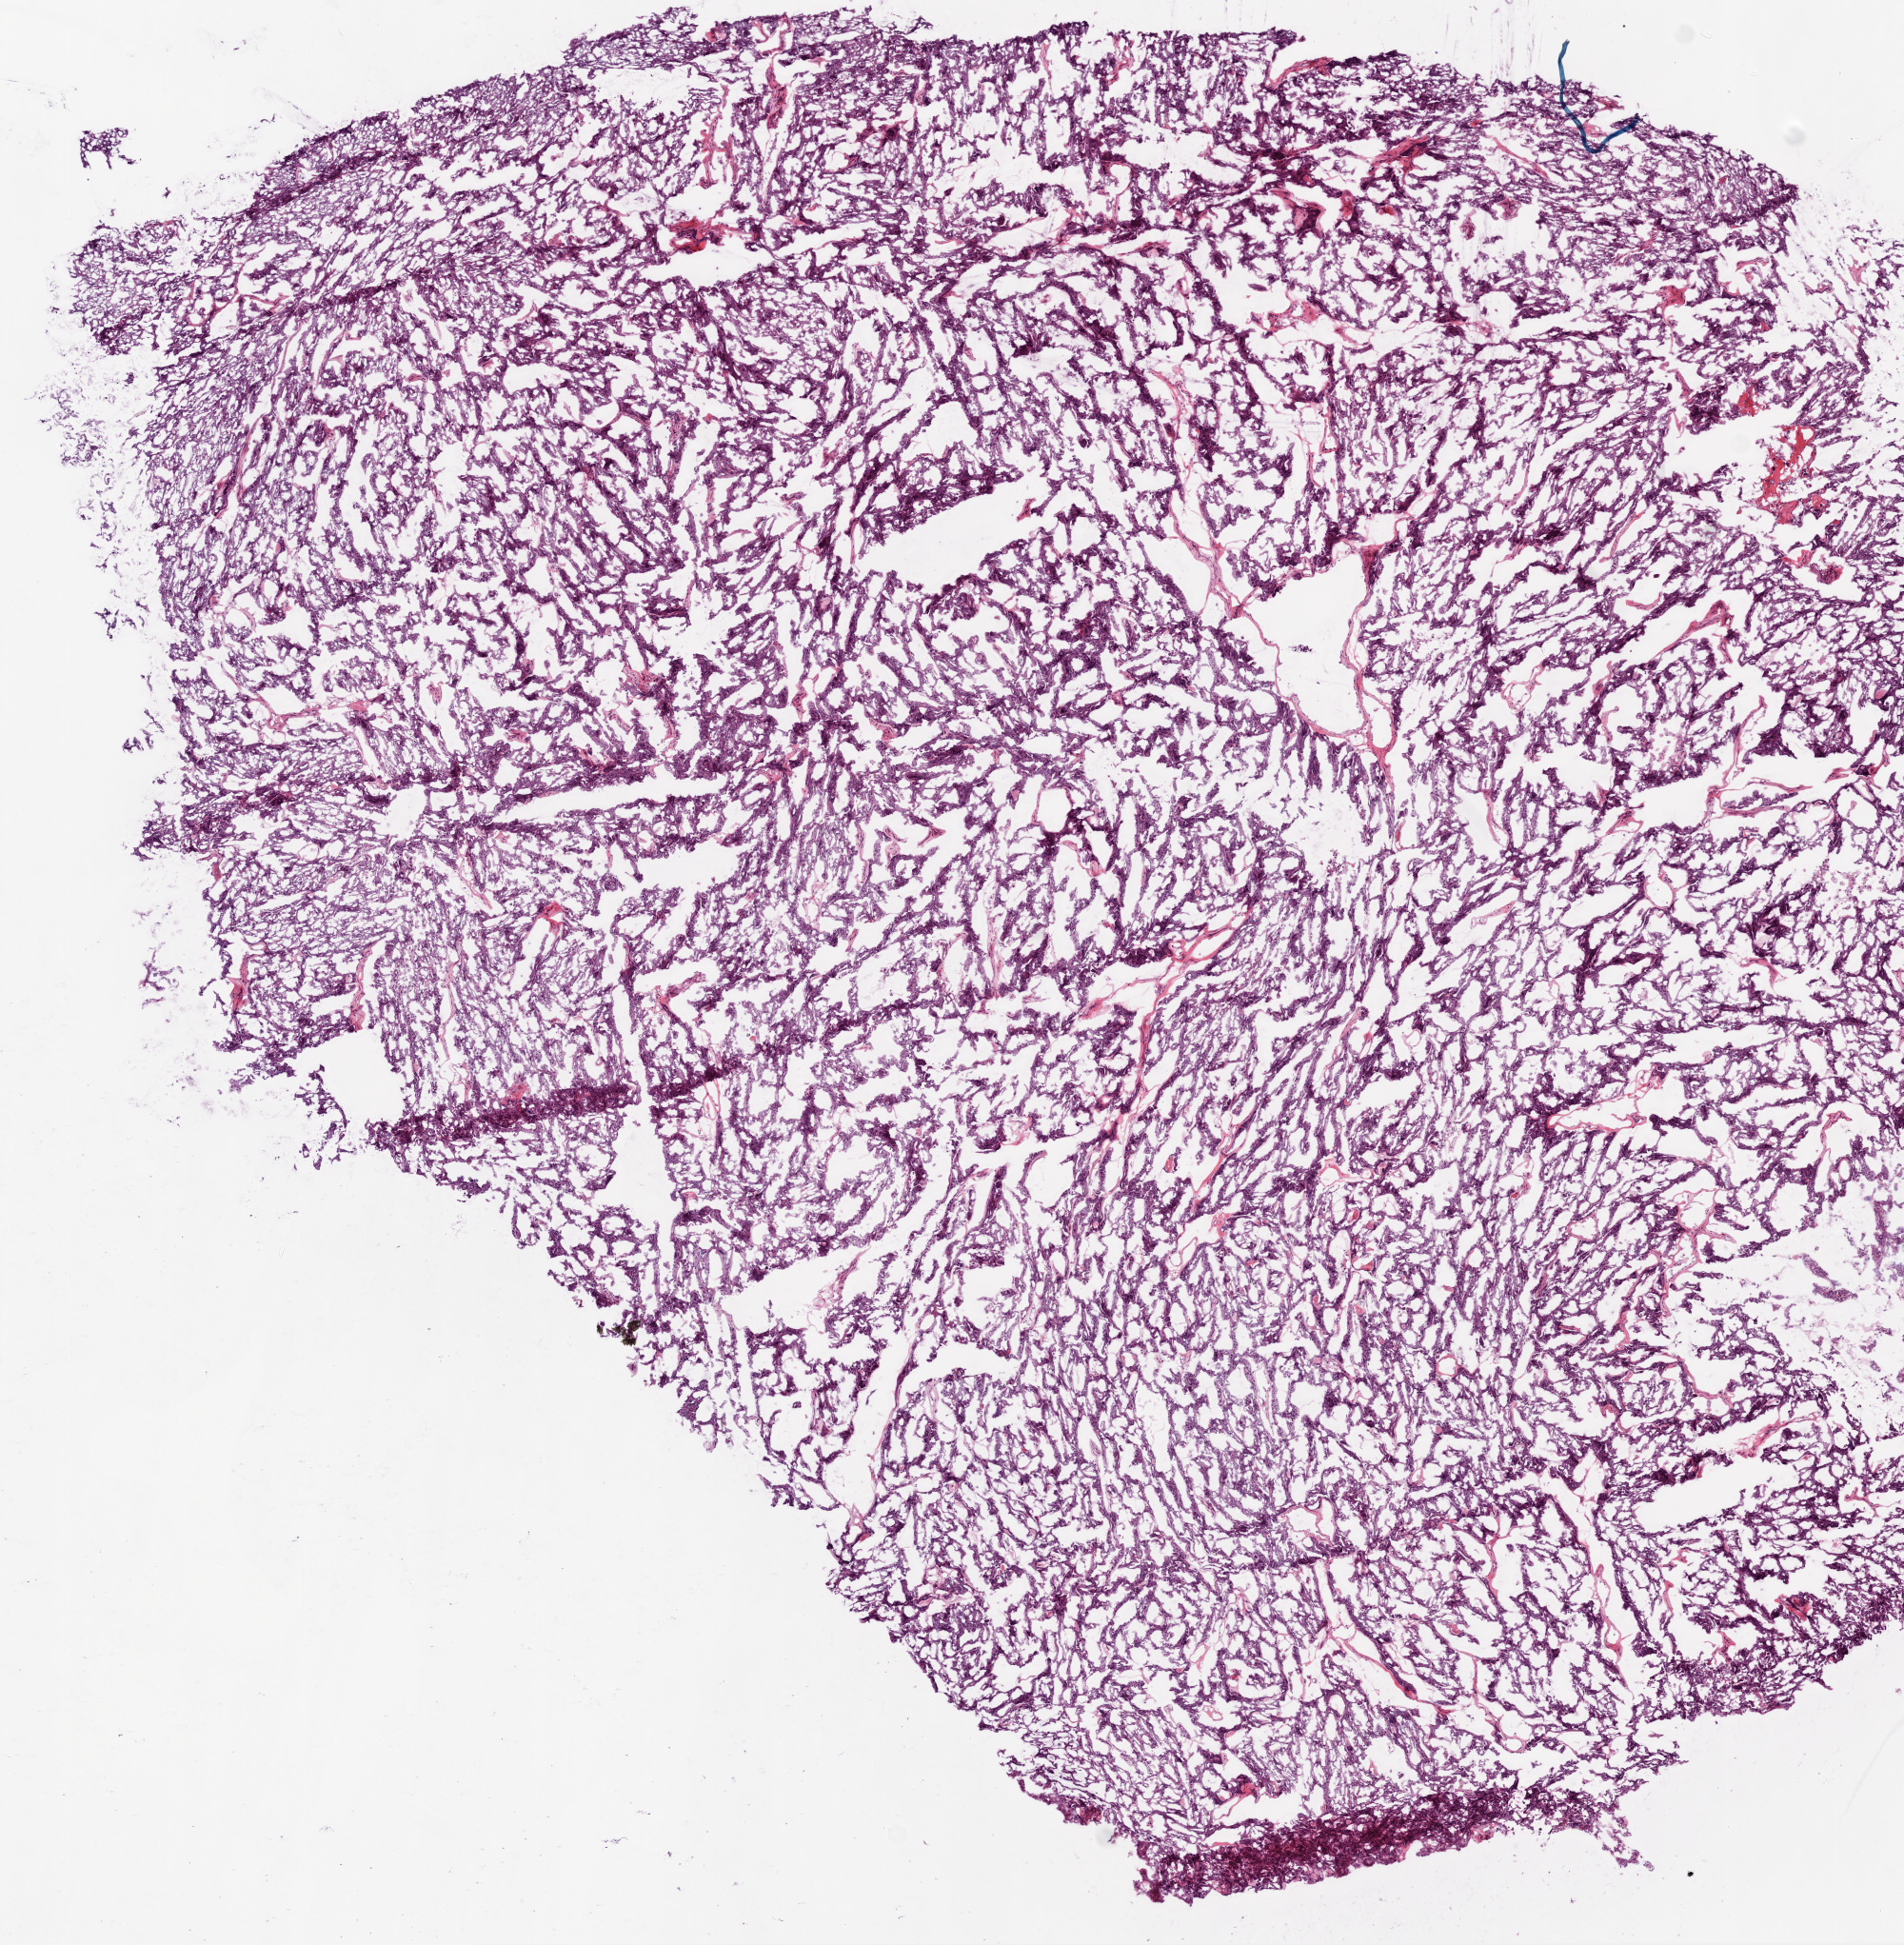
Whole-slide histology image, H&E-stained, shown as a low-resolution overview of the whole scanned area (about 8.0 x 8.2 mm). Frozen section from the top of the tissue portion. Primary tumour sample from the ovary. Patient: female, age at initial diagnosis 60 years.
Diagnosis: Serous cystadenocarcinoma, NOS.